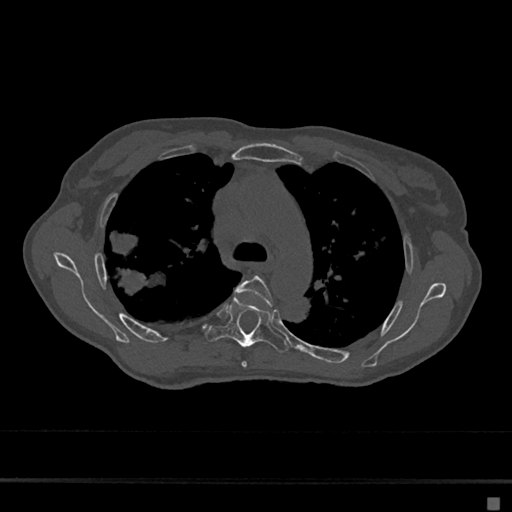
CT including the spine, one axial slice. Position 473 of 797 along the scan axis. Reconstruction kernel Br40s/3. 120 kVp. Bone window (W 1800 / L 400 HU). 512 × 512 image matrix. Female patient, age 68 years. Case-level facts recorded for this patient, not image findings: primary cancer: renal.
Outlined on this slice (semi-automatically segmented with operator editing):
- T4 vertebra: box from (x=236, y=276) to (x=274, y=368) px
- T5 vertebra: (x=206, y=297)–(x=289, y=352)